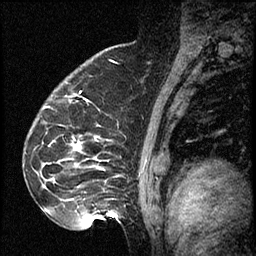
Breast MRI (dynamic contrast-enhanced), one sagittal slice; position 48 of 60 along the scan axis; dynamic contrast-enhanced series, image 2 of 2 at this slice position (ordered by acquisition); 1.5 T; TE 4.2 ms, TR 17.3 ms; 2 mm slice thickness; 256 × 256 image matrix, field of view 200 × 200 mm. Female patient. Case-level facts recorded for this patient, not image findings: setting: breast cancer imaged before/during neoadjuvant chemotherapy; receptor status: HR-positive, HER2-negative.
Structures marked on this image (semi-automatically segmented with operator editing):
- analysis volume of interest (the breast-tissue region the enhancement analysis was run in; not a lesion): bounding box <41,93,115,223> (left, top, right, bottom; pixels)
- tumour enhancement mask (voxels above the 100 % enhancement threshold inside the analysis volume of interest): <76,145,80,150>